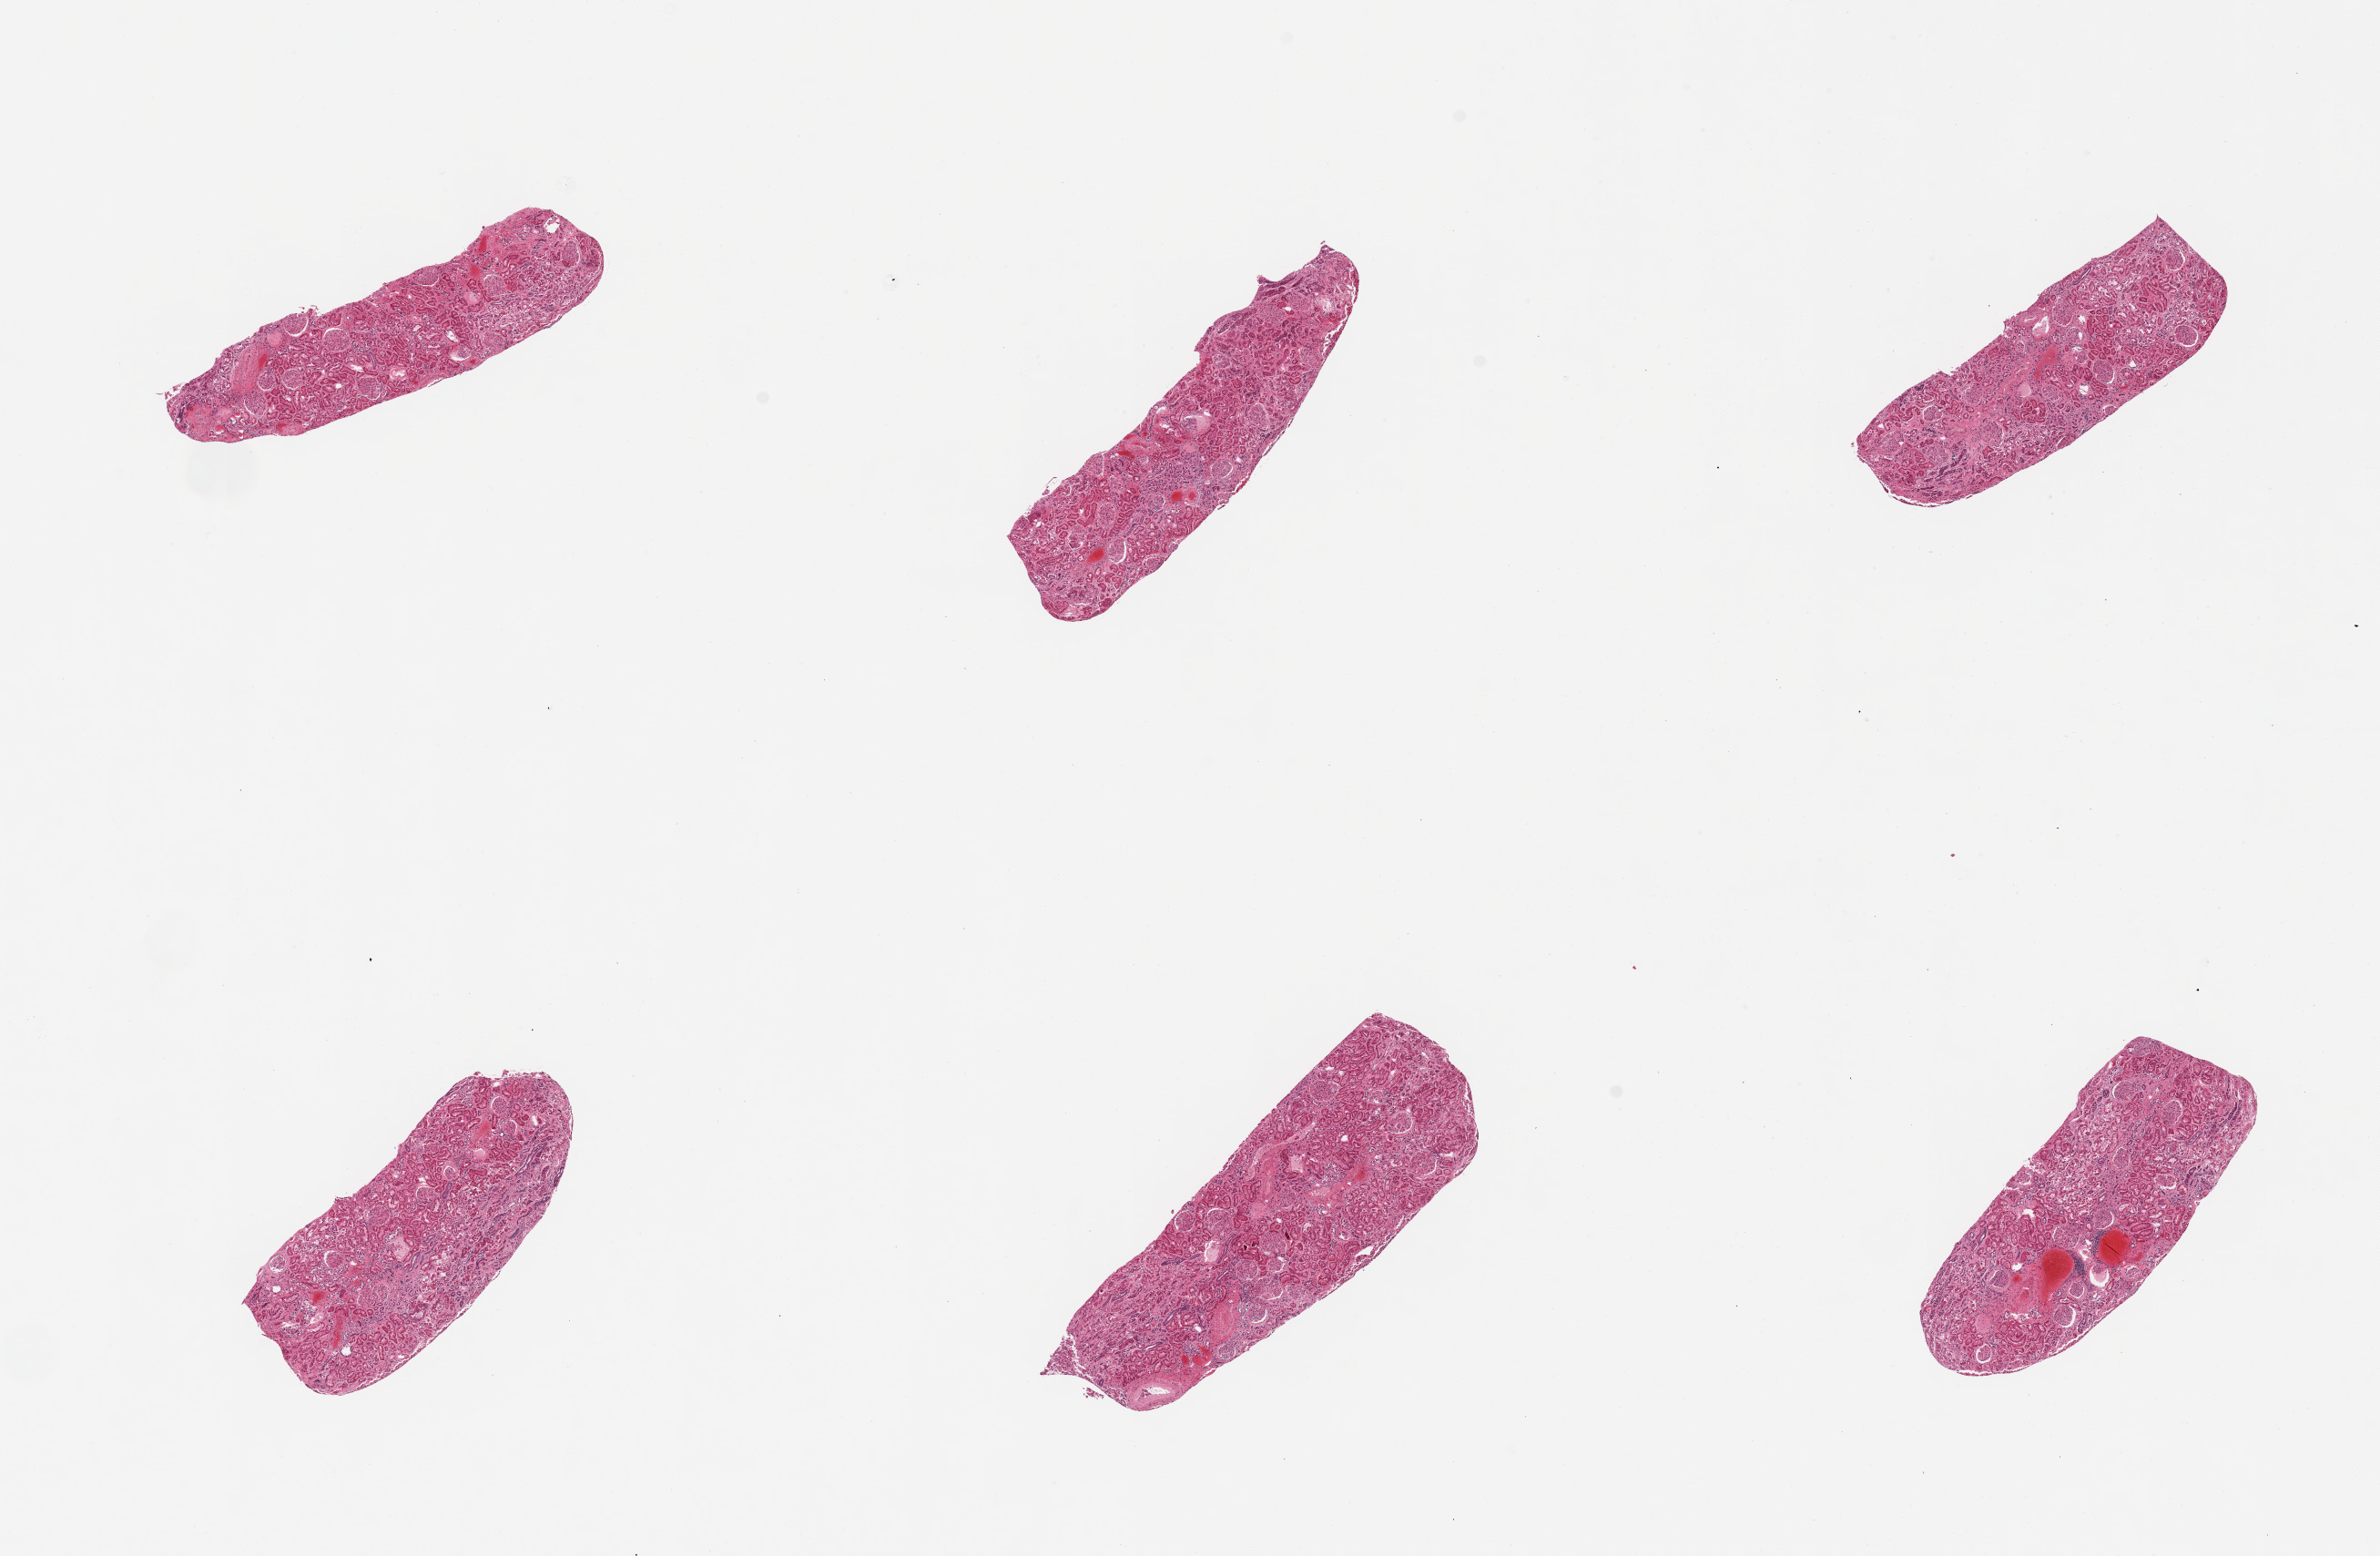
Haematoxylin and eosin whole-slide image, shown as a low-resolution overview of the whole scanned area (about 20.7 x 13.5 mm, from a 20x scan); PAXgene-fixed, paraffin-embedded tissue; target tissue: renal cortex; tissue donor sample. Donor: female.
Pathologist's review note for this sample: 6 pieces; renal cortex with mild arterio and arteriolonephrosclerosis and scattered sclerotic glomeruli, congestion.